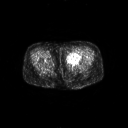
FDG PET of an extremity soft-tissue mass (from a PET/CT study), one axial slice. Position 18 of 267 along the scan axis. 3.27 mm slice thickness. 128 × 128 image matrix, field of view 700 × 700 mm. Female patient, age 47 years. Case-level facts recorded for this patient, not image findings: histological type: myxofibrosarcoma; grade: intermediate; site of the primary tumour: left thigh.
Outlined on this slice (expert contour drawn on MRI and transferred to this co-registered scan by the dataset authors):
- gross tumour volume including surrounding oedema: bounding box [x1, y1, x2, y2] px = [67, 52, 81, 64]
- gross tumour volume (mass): [67, 53, 80, 64]